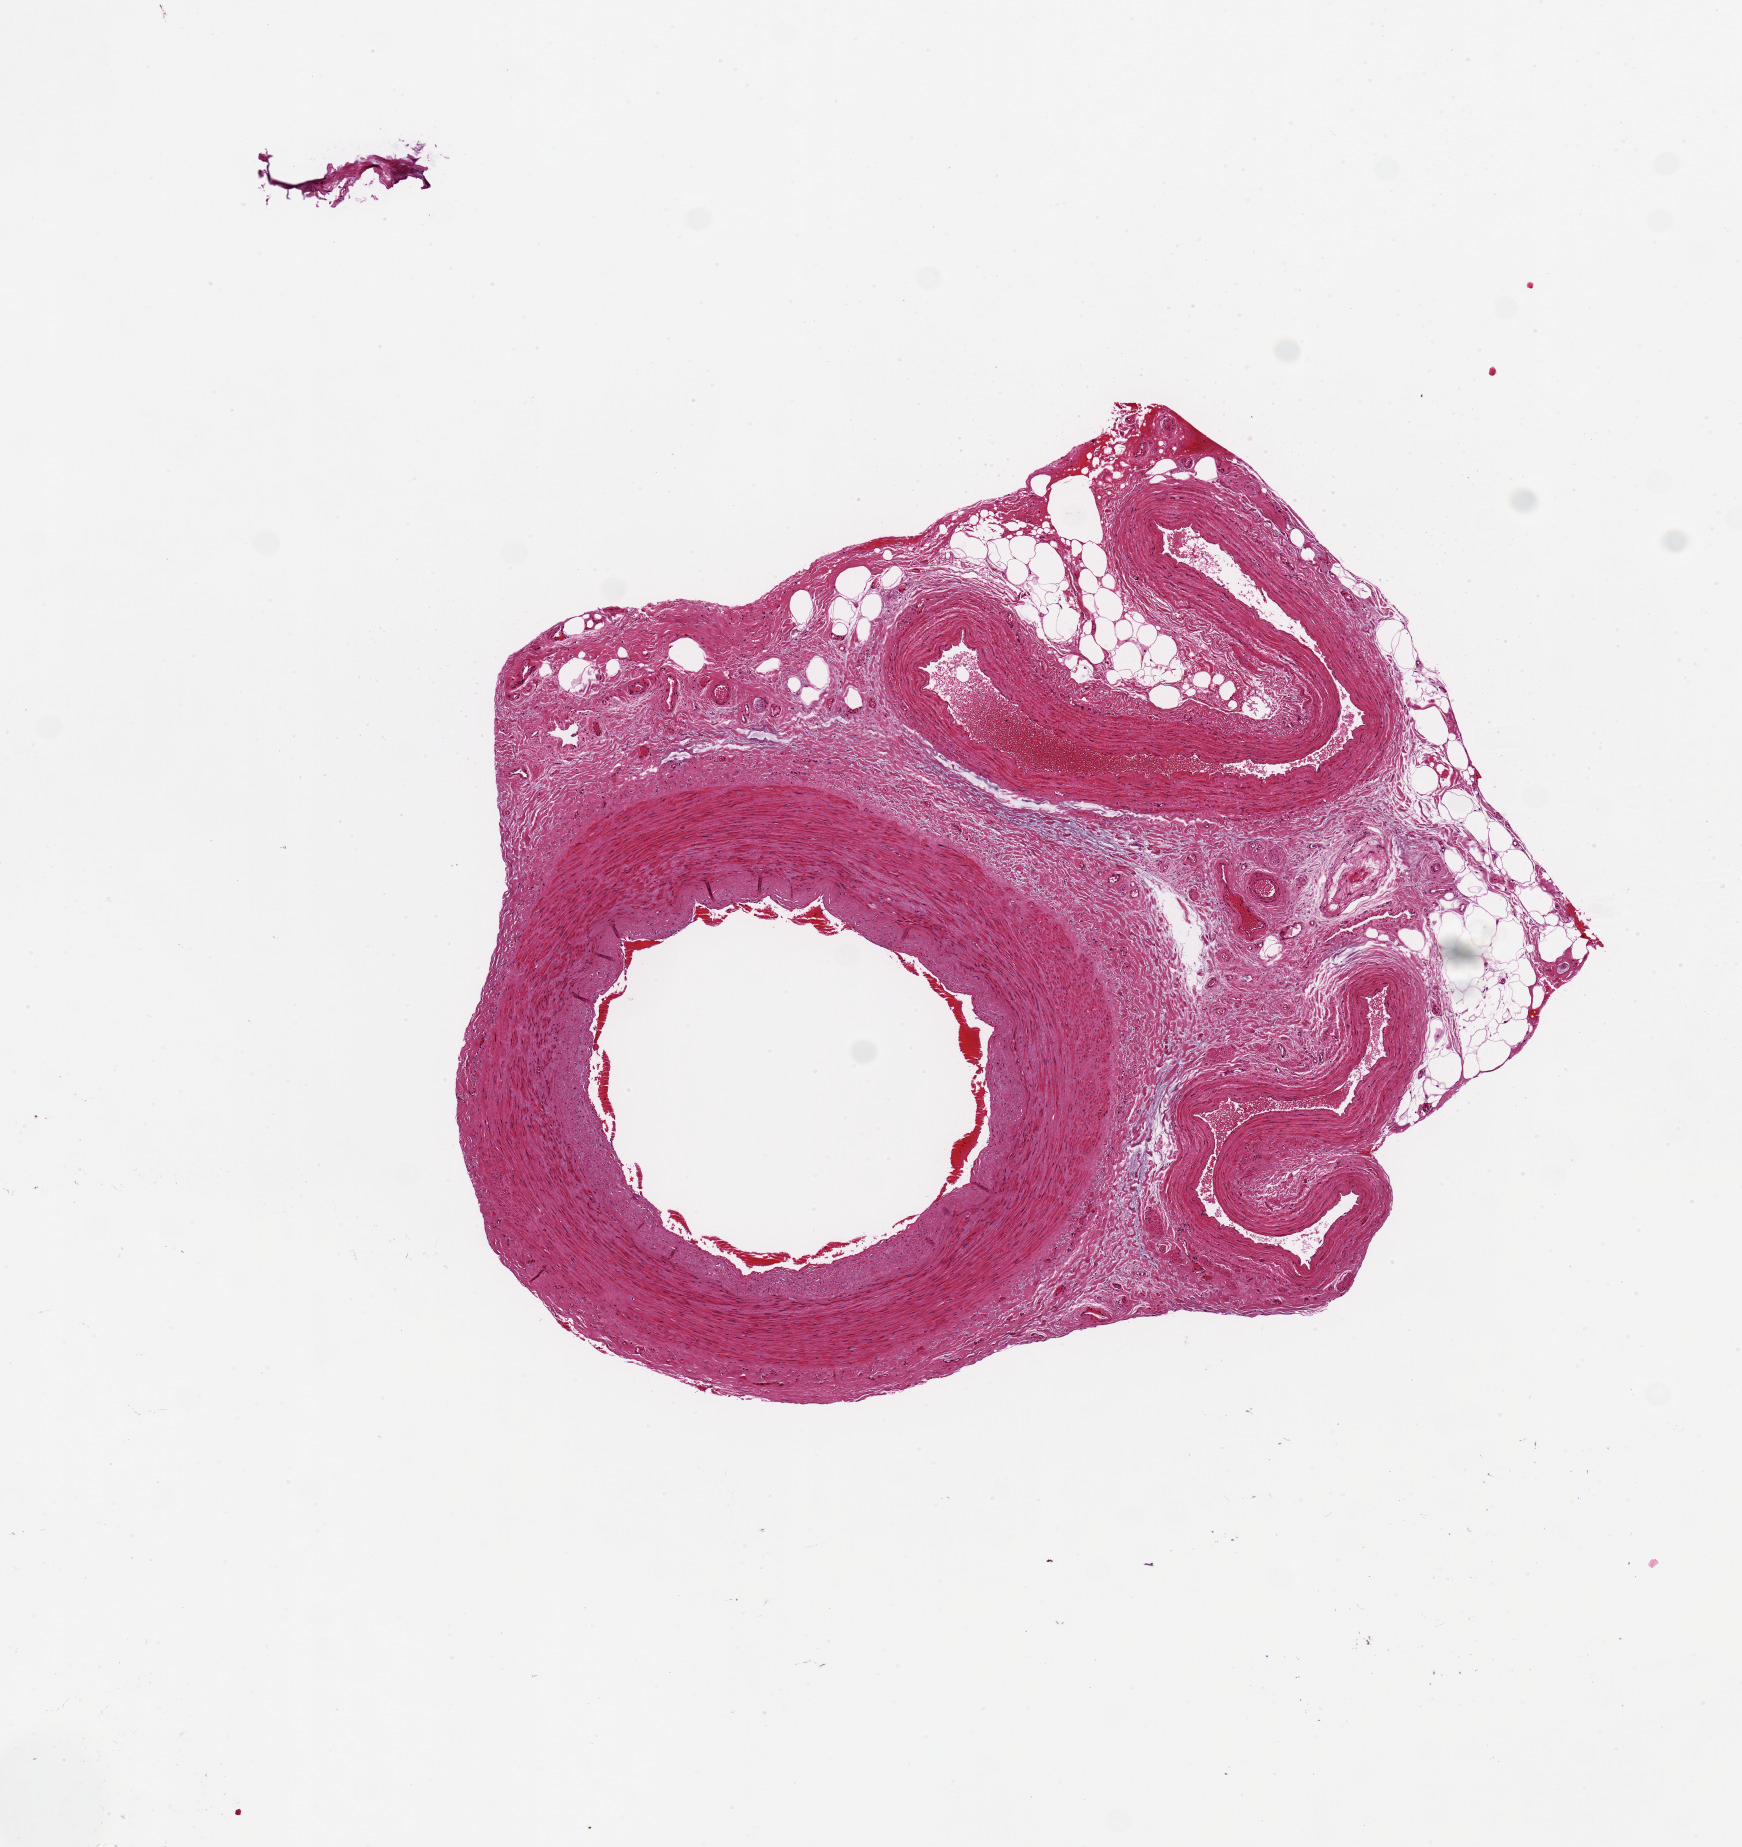
Haematoxylin and eosin whole-slide image, brightfield, a low-resolution overview of the entire scanned area, about 6.9 x 7.3 mm; PAXgene-fixed, paraffin-embedded tissue; section of tibial artery (target tissue); donor tissue sample. Donor: male.
- reviewer comment on this tissue sample: Artery plus 2 veins; minimal intimall thickening